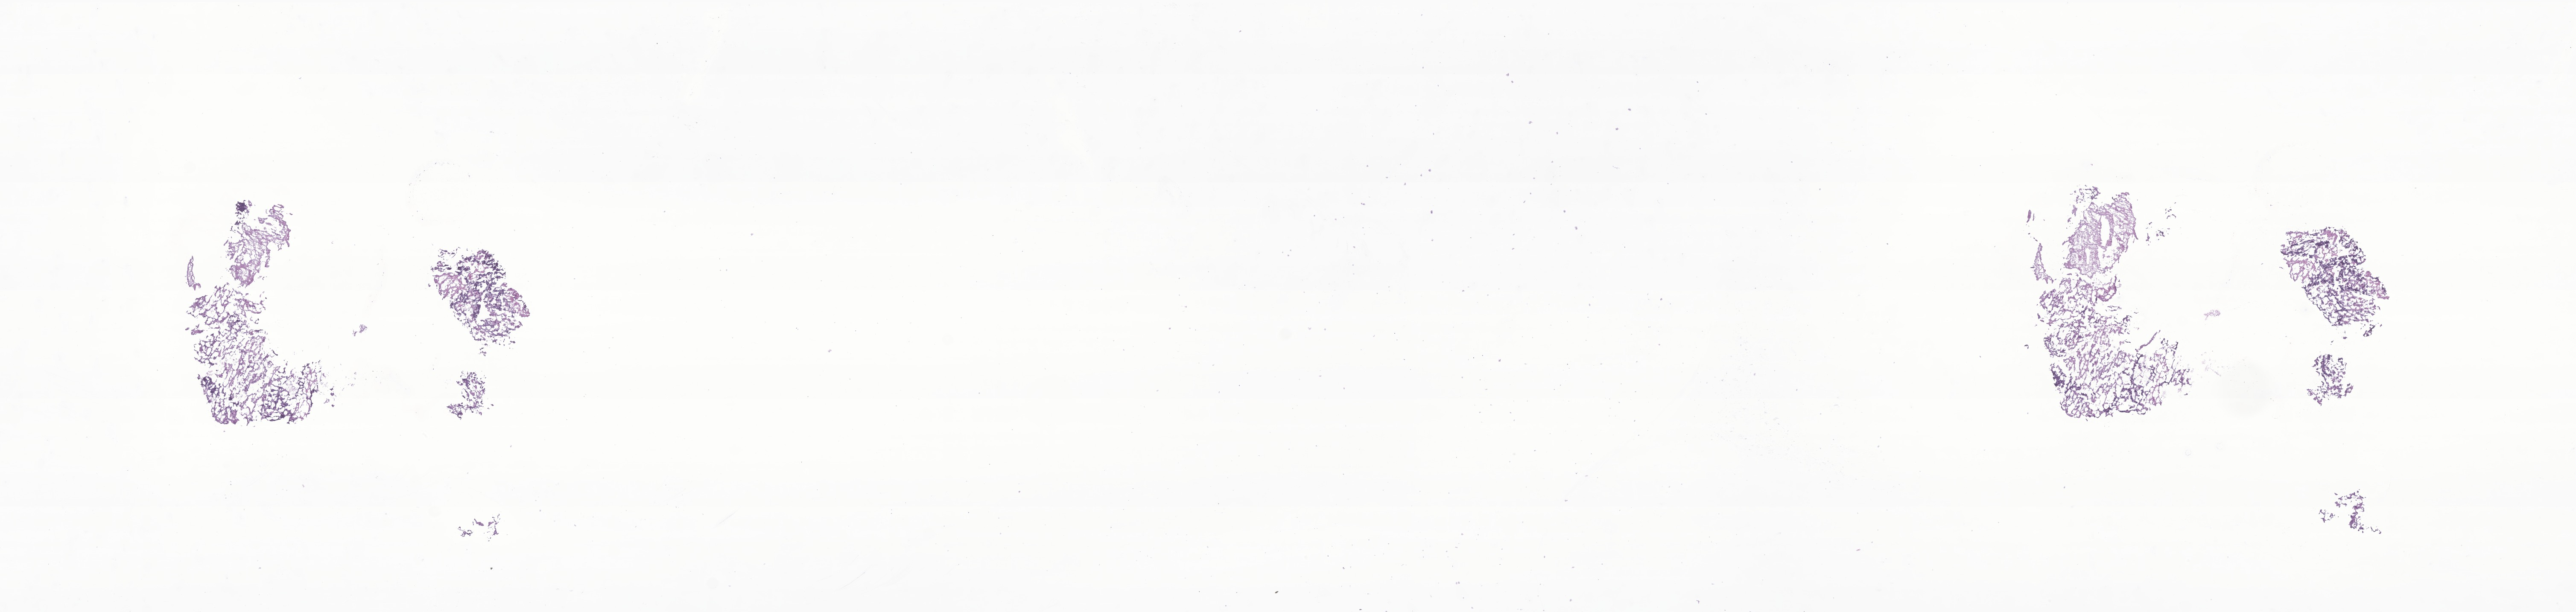
Whole-slide image, haematoxylin and eosin stain of tumor tissue from the brain — shown as a low-resolution overview of the whole scanned area (about 25.4 x 6.0 mm); frozen section. Patient female; age 660 days (about 1.8 years).
Recorded diagnosis: CNS embryonal tumor, NOS.